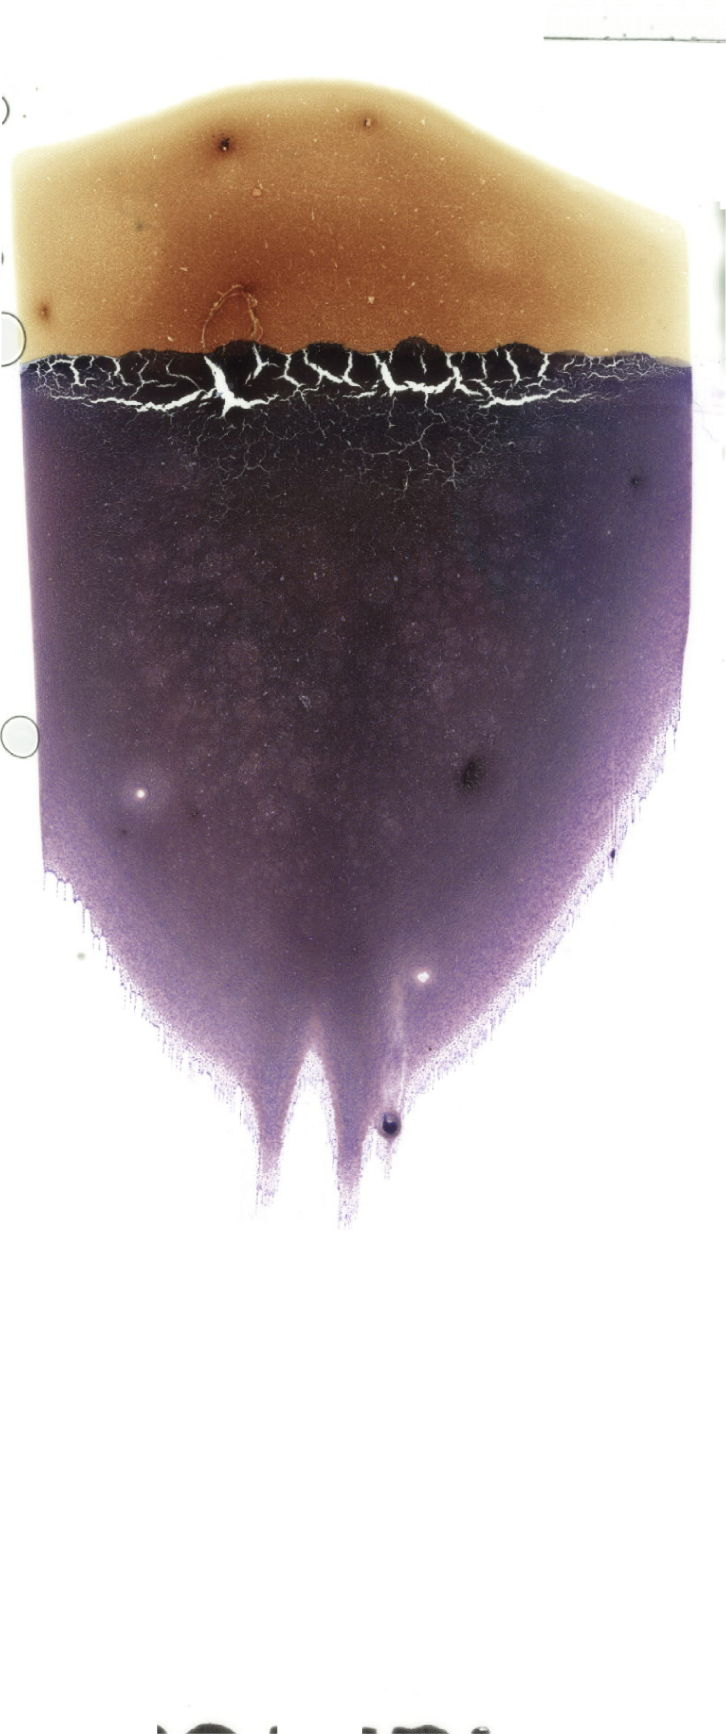
Whole-slide image of a May-Grünwald–Giemsa-stained bone marrow aspirate smear, shown as a low-resolution overview of the whole scanned area (about 20.6 x 49.2 mm). Patient sex: female.
* diagnosis: Acute Myelomonocytic Leukemia